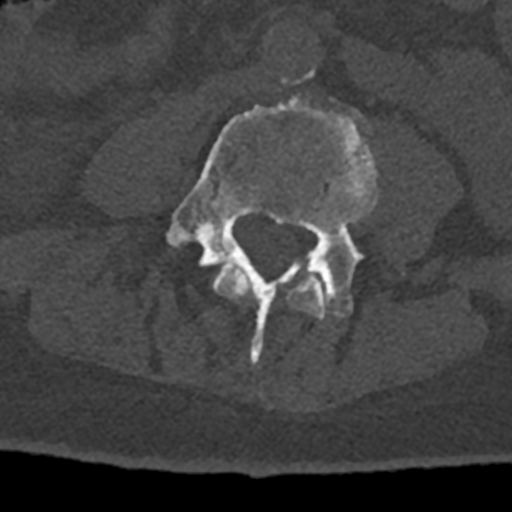
CT including the spine, one axial slice. Slice 270 of 797 in the series (ordered by position). Reconstruction kernel Br40s/3. Bone window (W 1800 / L 400 HU). 0.5 mm slice thickness. 512 × 512 image matrix, field of view 160 × 160 mm. Male patient, age 74 years. From the clinical record (not read from this slice): primary cancer: renal.
Annotated regions visible in this slice (semi-automatic segmentation, software-assisted and operator-edited):
- L3 vertebra: bounding box (x1, y1, x2, y2) in pixels: (212, 263, 328, 319)
- L4 vertebra: (165, 82, 377, 361)